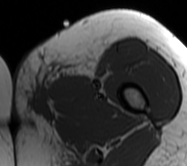
MRI of an extremity soft-tissue mass, one axial slice; position 13 of 62 along the scan axis; MR volume resampled by the dataset authors to the PET/CT grid (not the native acquisition matrix); 3.27 mm slice thickness; 187 × 166 image matrix. Female patient. From the clinical record (not read from this slice): histological type: leiomyosarcoma; grade: high; site of the primary tumour: groin.
Structures marked on this image (expert contour drawn on MRI and transferred to this co-registered scan by the dataset authors):
- gross tumour volume including surrounding oedema: bounding box [x1, y1, x2, y2] px = [11, 51, 94, 121]